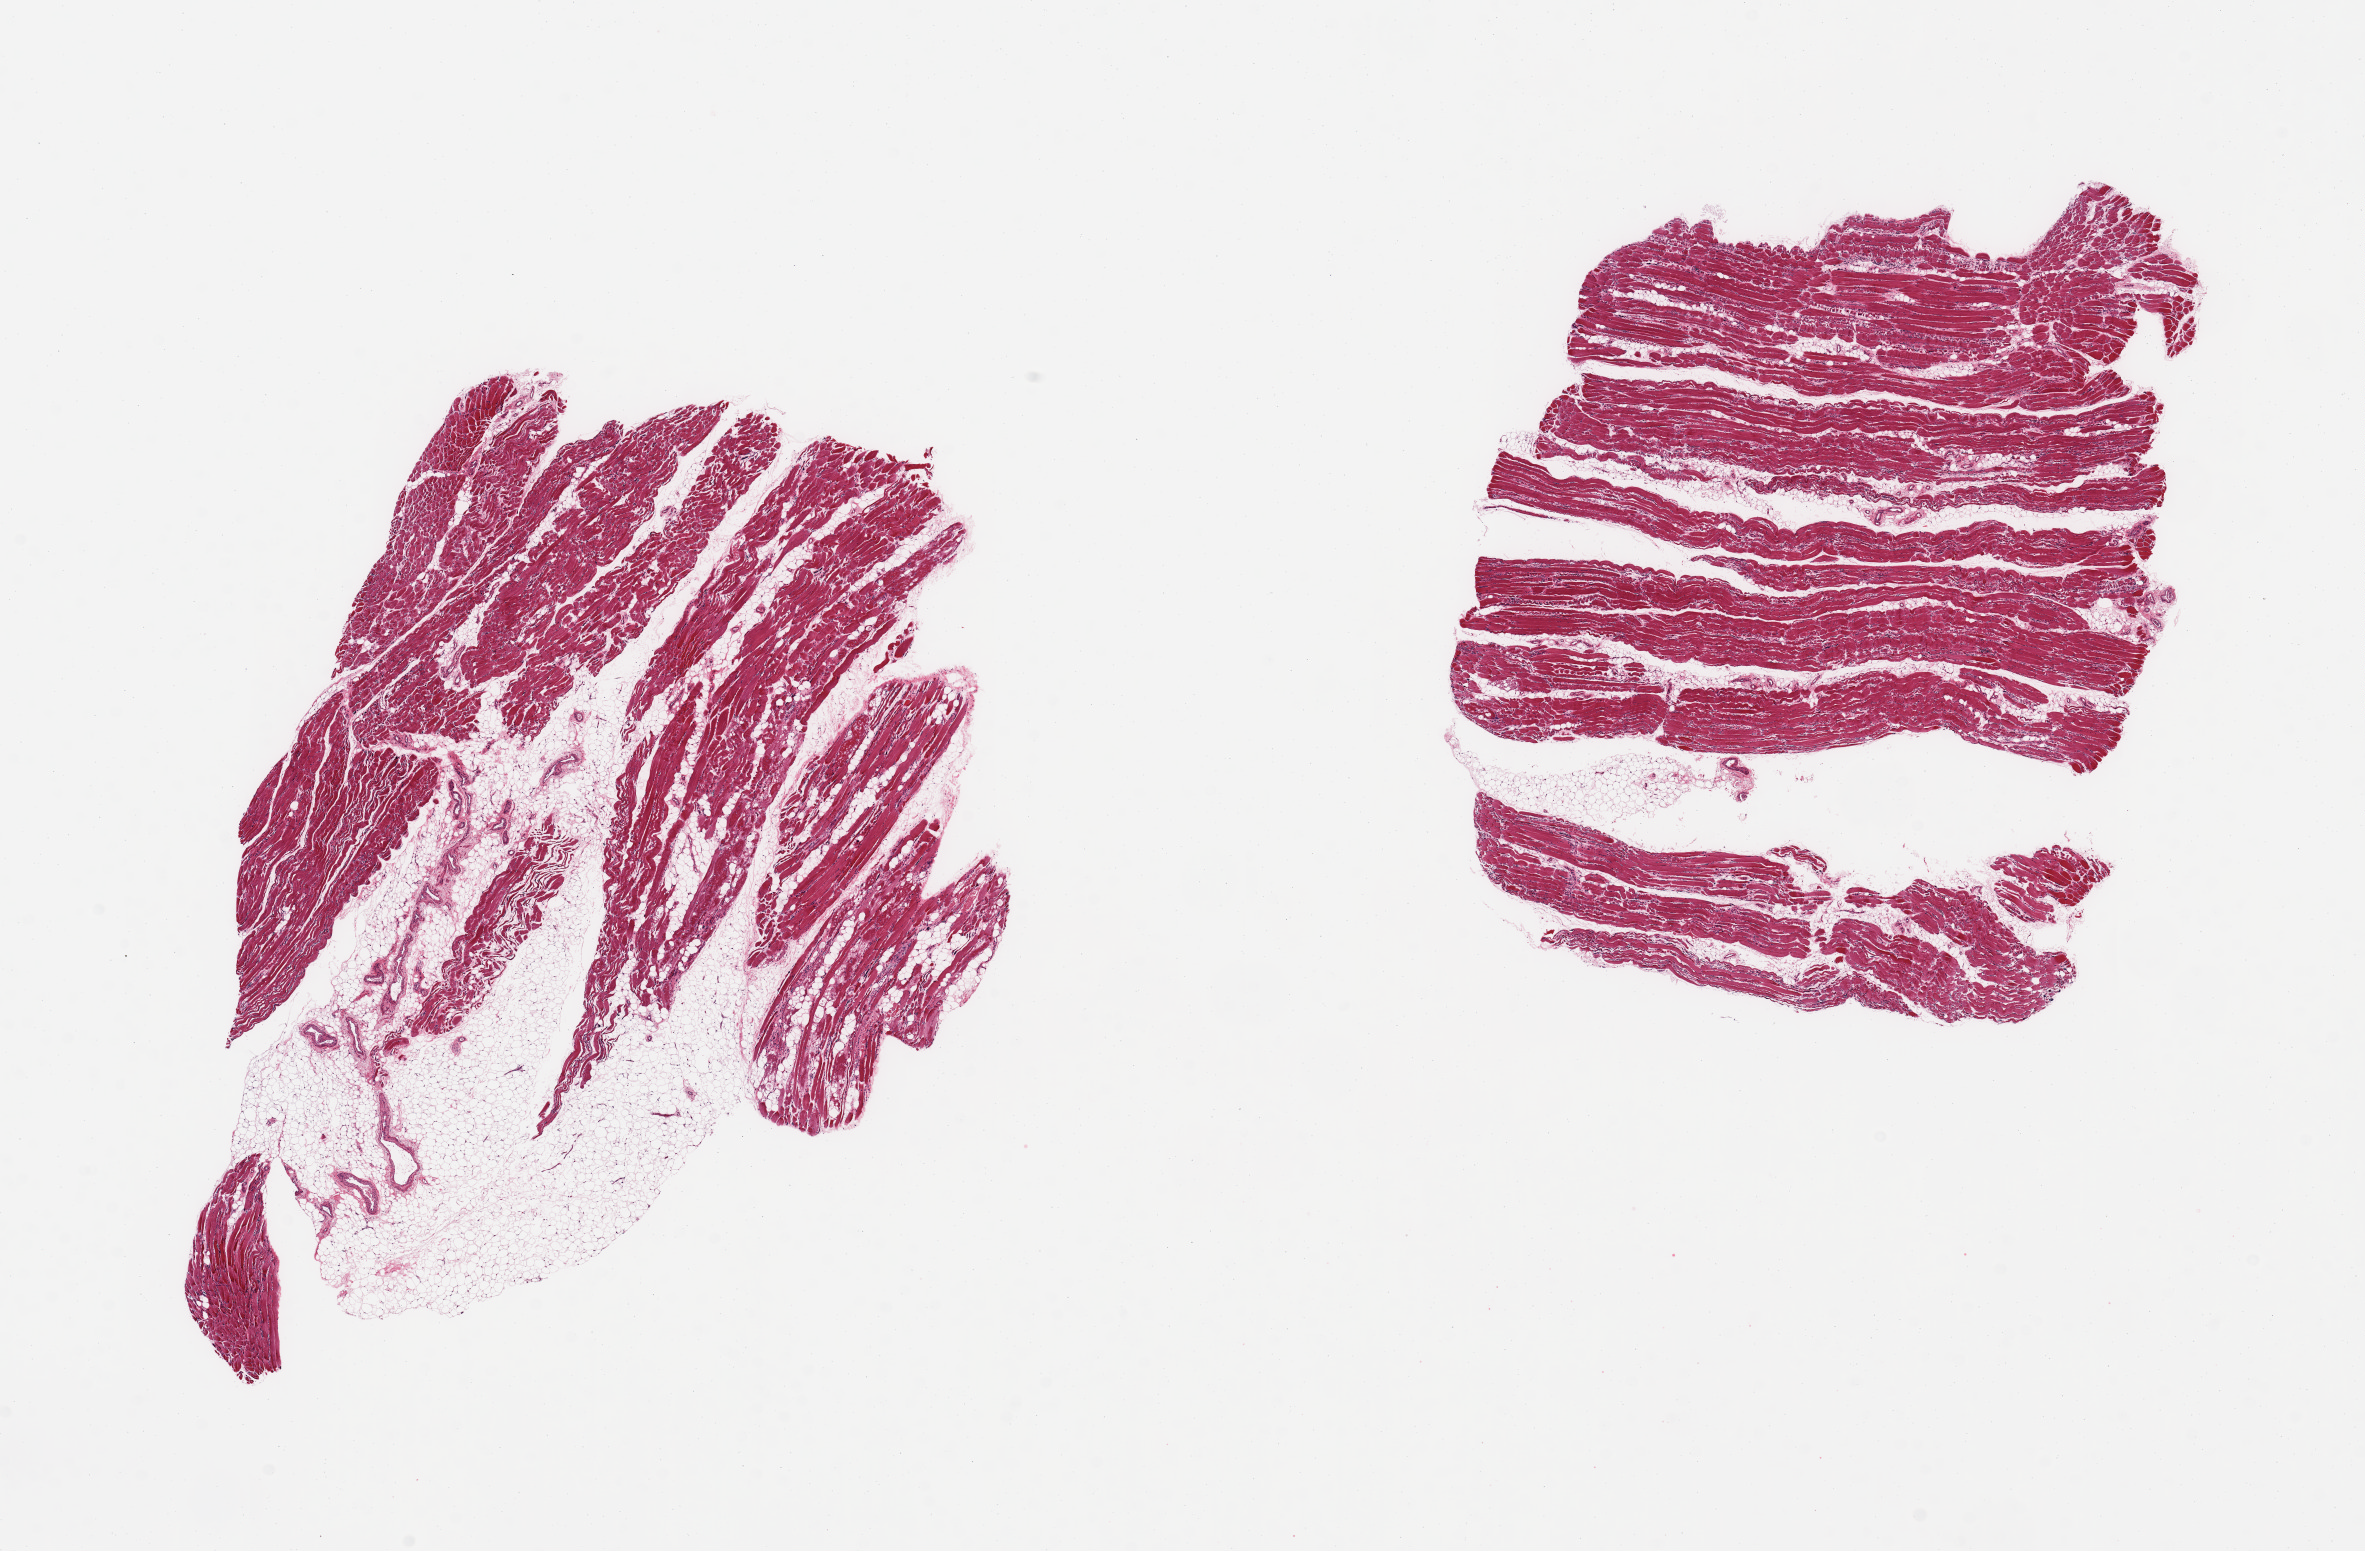
Whole-slide image, haematoxylin and eosin stain, brightfield — low-resolution overview of the scanned area, about 18.7 x 12.3 mm (acquisition: 20x scan); PAXgene-fixed paraffin-embedded (PFPE) section; target tissue: skeletal muscle; donor tissue sample. Female donor.
- reviewer comment on this tissue sample: 2 pieces; moderate atrophy; 10% & 20% internal fat